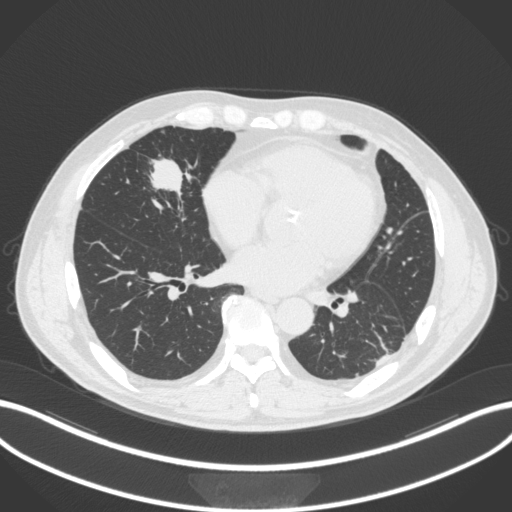
Chest CT, one axial slice. Position 113 of 399 along the scan axis. Reconstruction kernel B31f. 120 kVp. Lung window (W 1500 / L -600 HU). 1 mm slice thickness. 512 × 512 image matrix. Male patient, age 59 years. From the clinical record (not read from this slice): clinical TNM (as recorded): T2a N1 M0.
Annotated regions visible in this slice (bounding box drawn by a radiologist):
- lung tumour (recorded histology: adenocarcinoma): box from (x=140, y=151) to (x=197, y=200) px